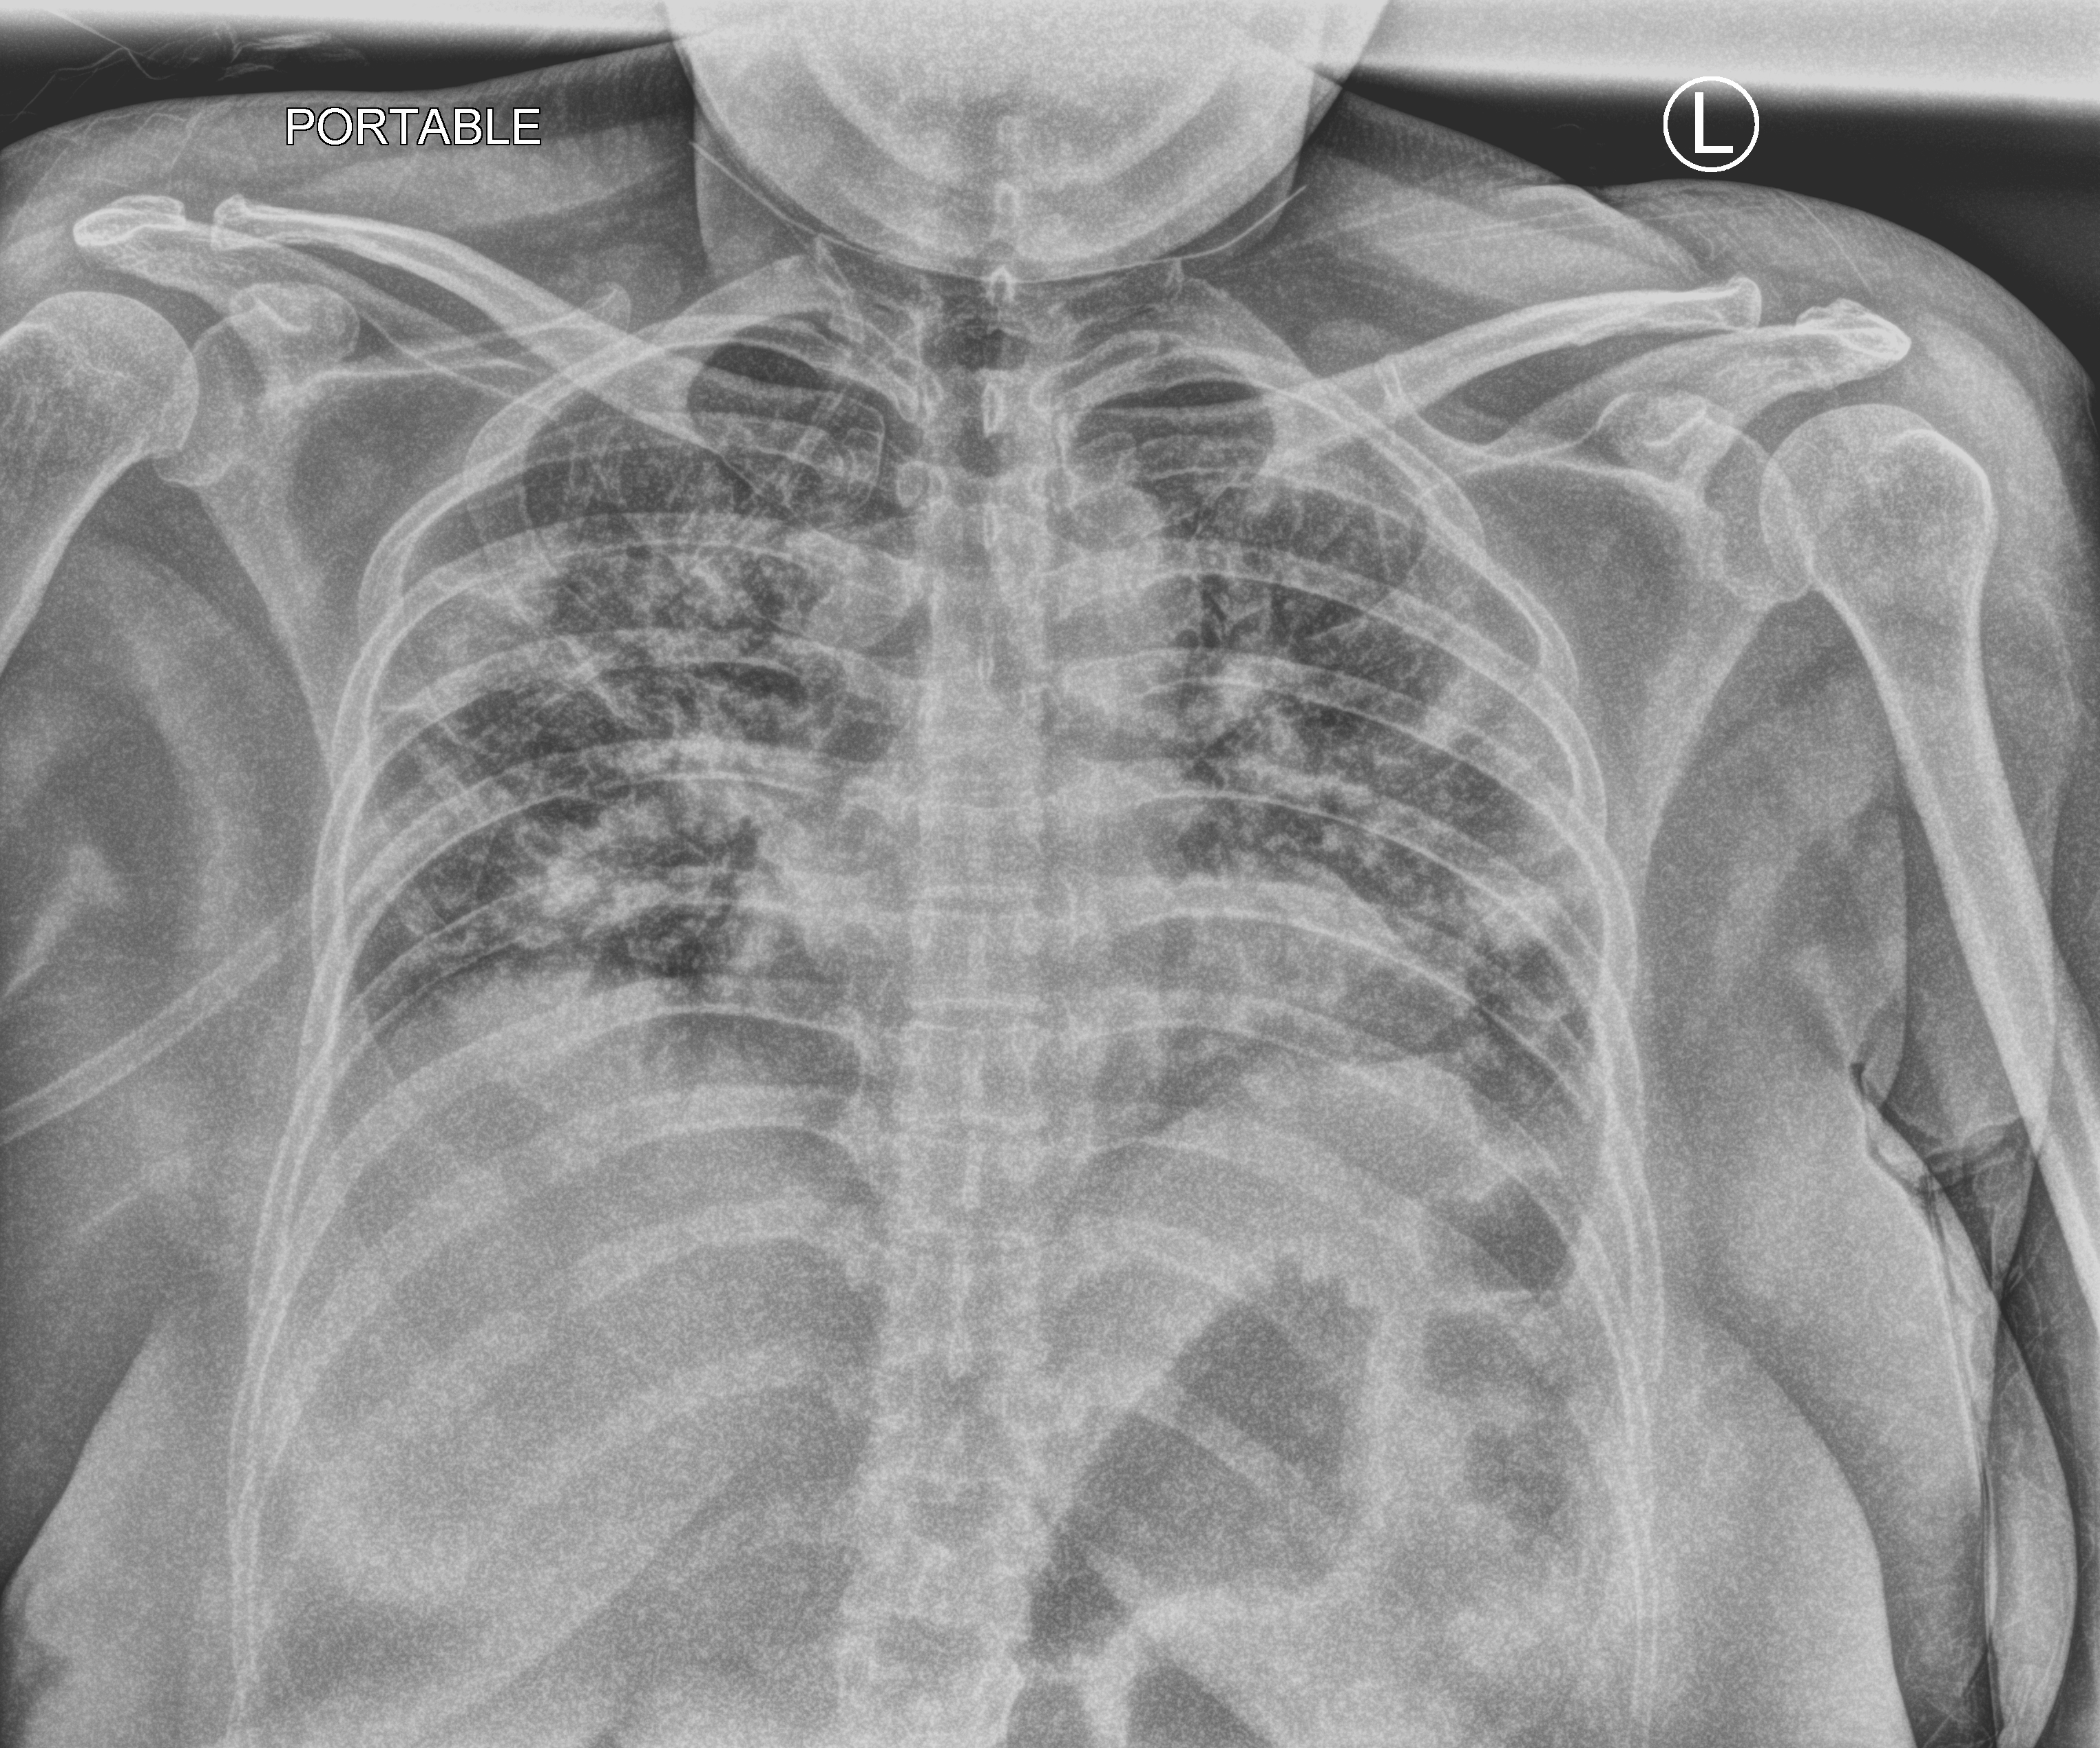
Chest X-ray (portable), anteroposterior (AP) projection. Patient hospitalised with COVID-19; female, aged 18–59 years.
Admission-level facts for this patient (not findings on this image; timing relative to this image not recorded):
- other chronic lung disease (admission record): no
- mechanically ventilated during this hospital stay: yes